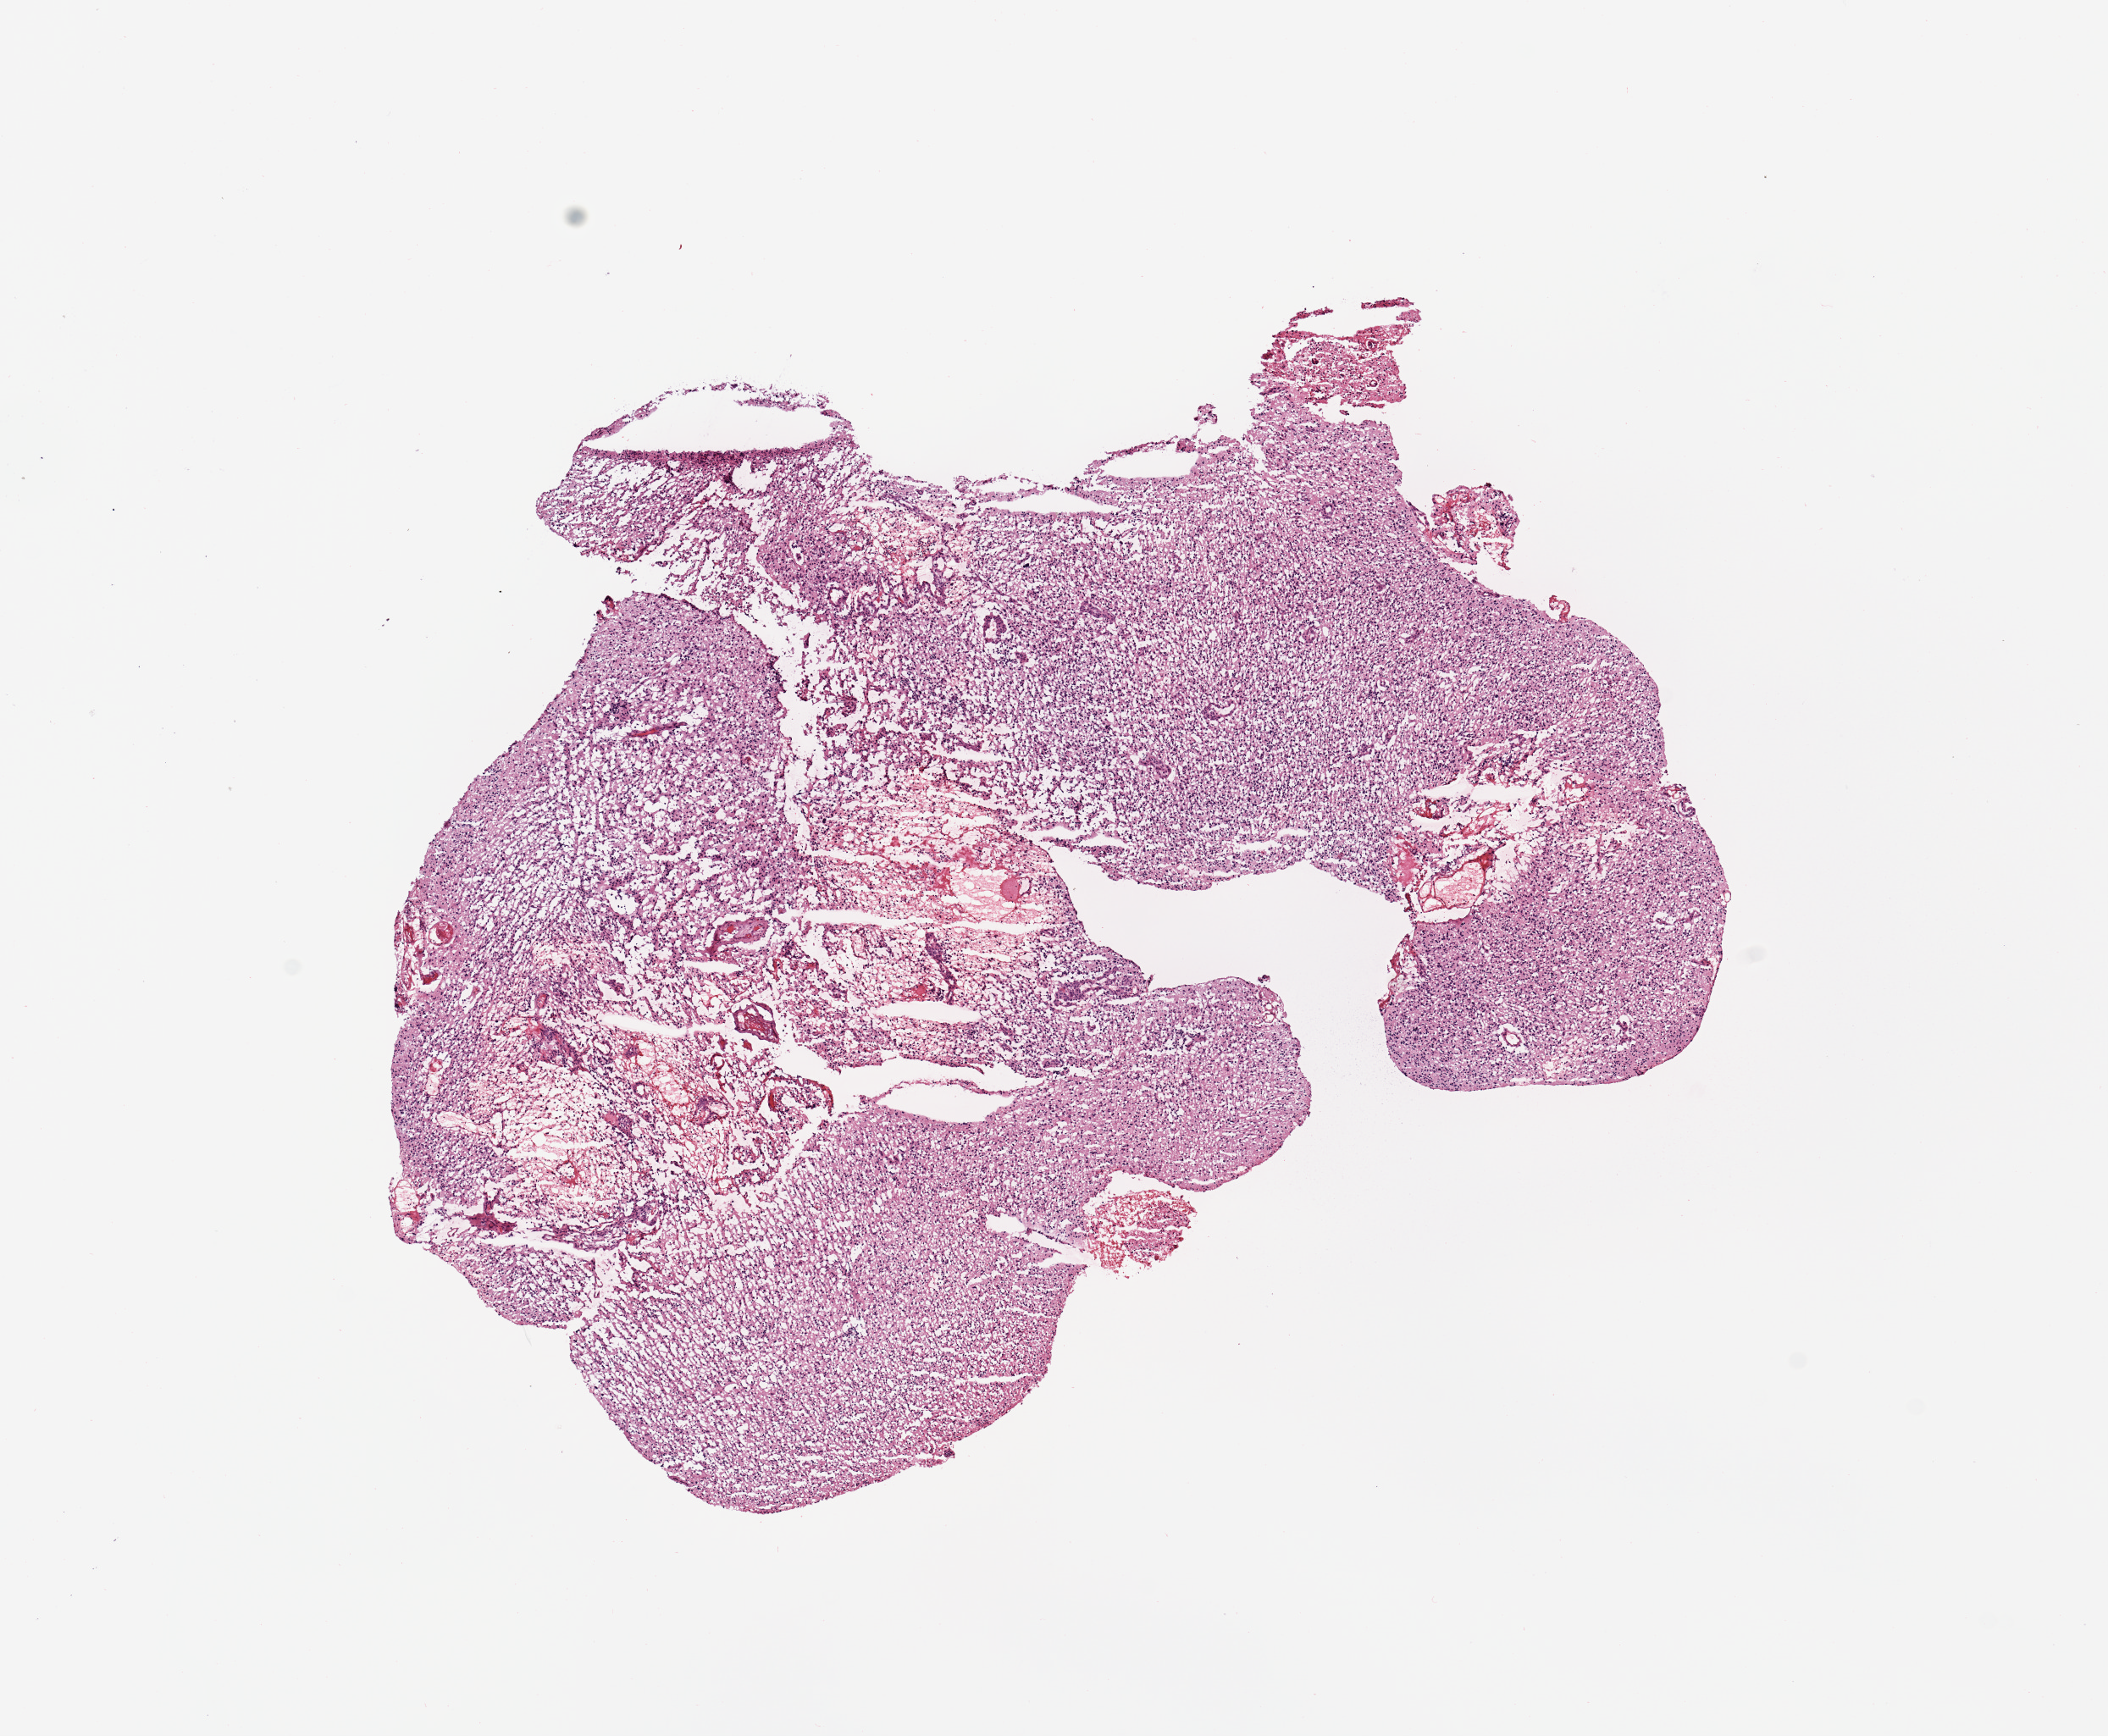
Digitized H&E tissue section (whole slide), whole scanned area (about 9.8 x 8.1 mm, from a 20x scan) shown as a low-resolution overview. Brain, tumour tissue. Patient: male, age 62 years.
* patient diagnosis (cohort enrolment): glioblastoma multiforme (brain)
* primary tumour site (as recorded): occipital lobe